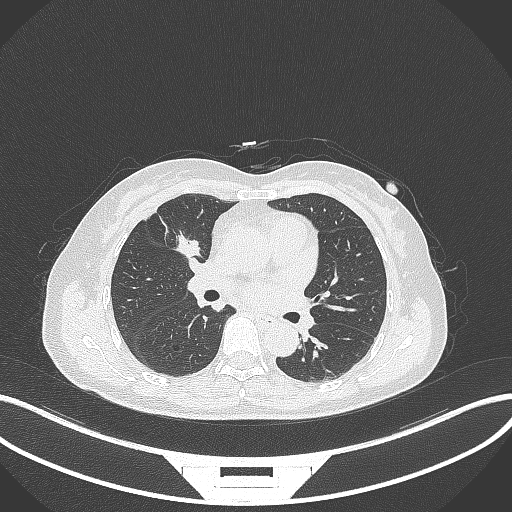
Chest CT, one axial slice. Slice 162 of 284 in the series (ordered by position). Lung window (W 1500 / L -600 HU). 512 × 512 image matrix, field of view 400 × 400 mm. Female patient, age 51 years. From the clinical record (not read from this slice): clinical TNM (as recorded): T1c N0 M0.
Annotated regions visible in this slice (bounding box drawn by a radiologist):
- lung tumour (recorded histology: adenocarcinoma): box from (x=173, y=228) to (x=207, y=259) px